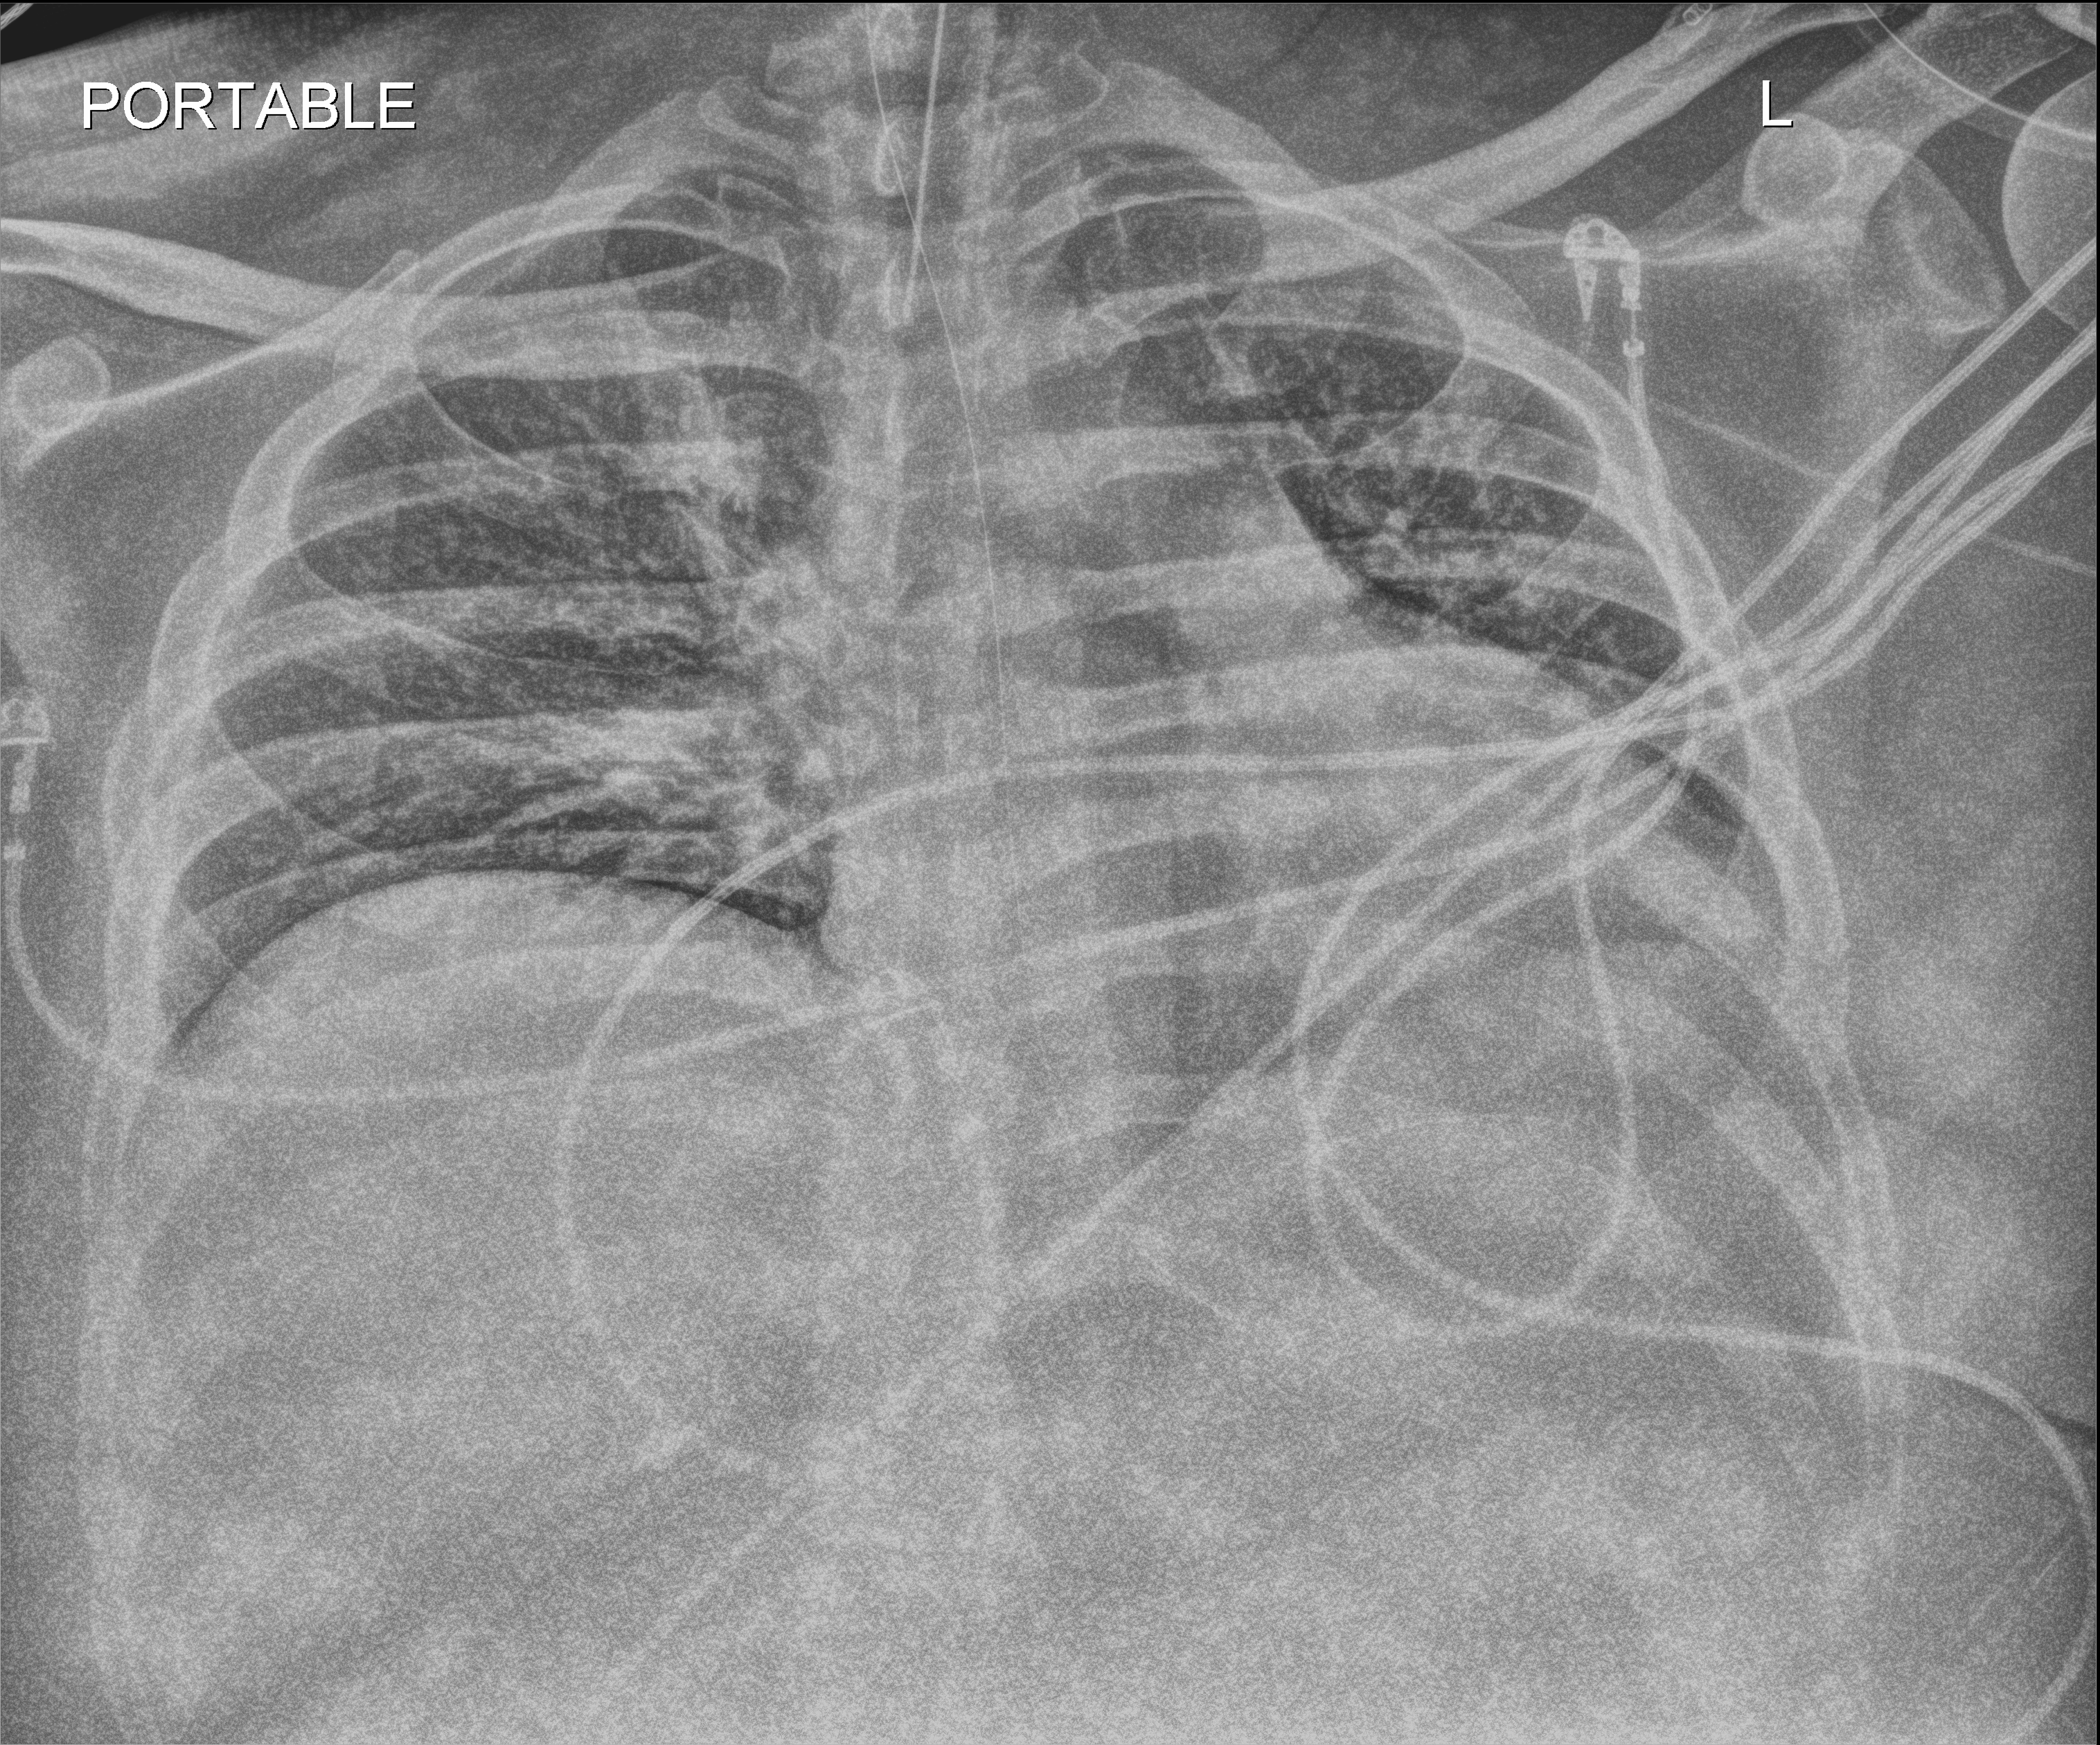
Chest X-ray (portable), anteroposterior (AP) projection. Patient hospitalised with COVID-19; male, aged 18–59 years.
From the hospital-stay record, not from the radiograph (when in the stay this image was taken is not recorded): other chronic lung disease (admission record): yes.